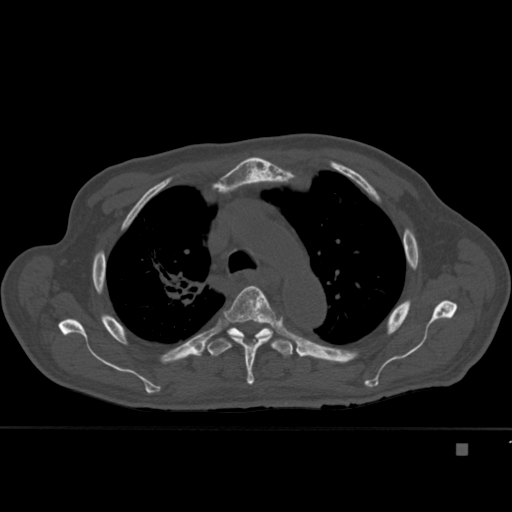
CT including the spine, one axial slice. Position 316 of 451 along the scan axis. Bone window (W 1800 / L 400 HU). 512 × 512 image matrix, field of view 378 × 378 mm. Male patient, age 75 years. From the clinical record (not read from this slice): primary cancer: prostate.
Structures marked on this image (semi-automatic segmentation, software-assisted and operator-edited):
- T4 vertebra: box from (x=223, y=286) to (x=277, y=385) px
- T5 vertebra: (x=207, y=327)–(x=293, y=357)